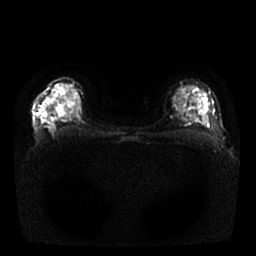
Breast MRI, one axial slice. Slice 15 of 25 in the series (ordered by position). Diffusion-weighted series; image 2 of 4 stored at this slice position (different b-values; order by instance number). 1.5 T. 4 mm slice thickness. 256 × 256 image matrix. Female patient.
Outlined on this slice (outlined manually by an expert reader):
- tumour on diffusion-weighted imaging: bounding box <43,114,46,117> (left, top, right, bottom; pixels)